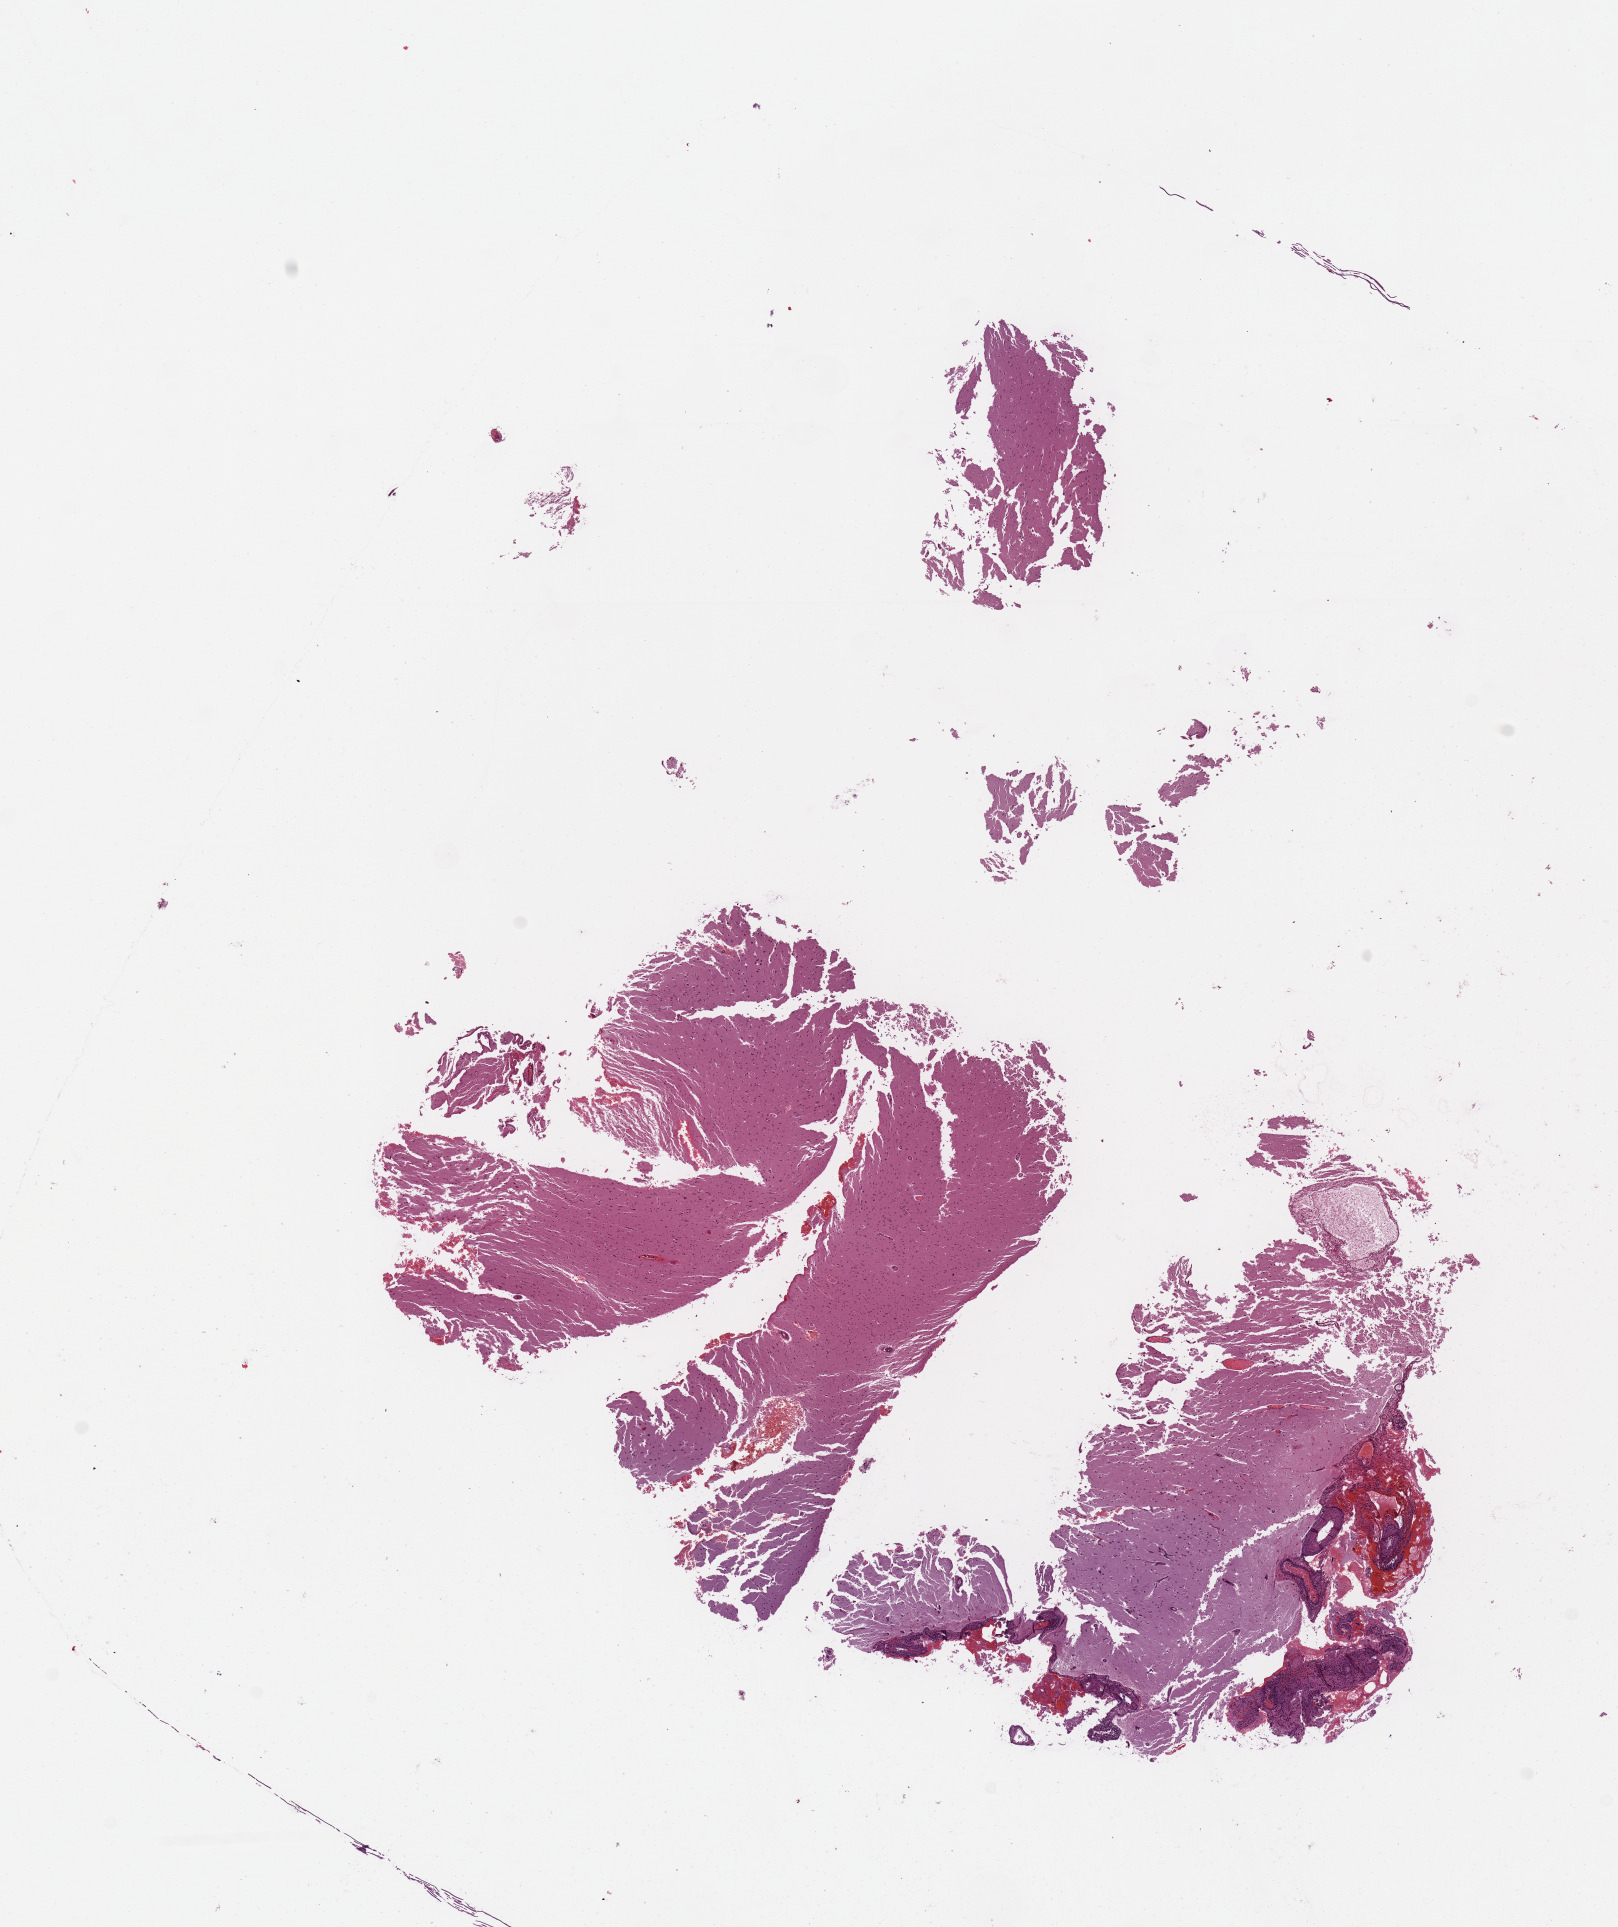
Whole-slide histology image, H&E — a low-resolution overview of the entire scanned area, about 12.8 x 15.2 mm (from a 20x scan), tumour tissue sample, brain. Patient: male, age 49 years.
• histologic diagnosis: Glioblastoma
• primary tumour site (as recorded): frontal lobe